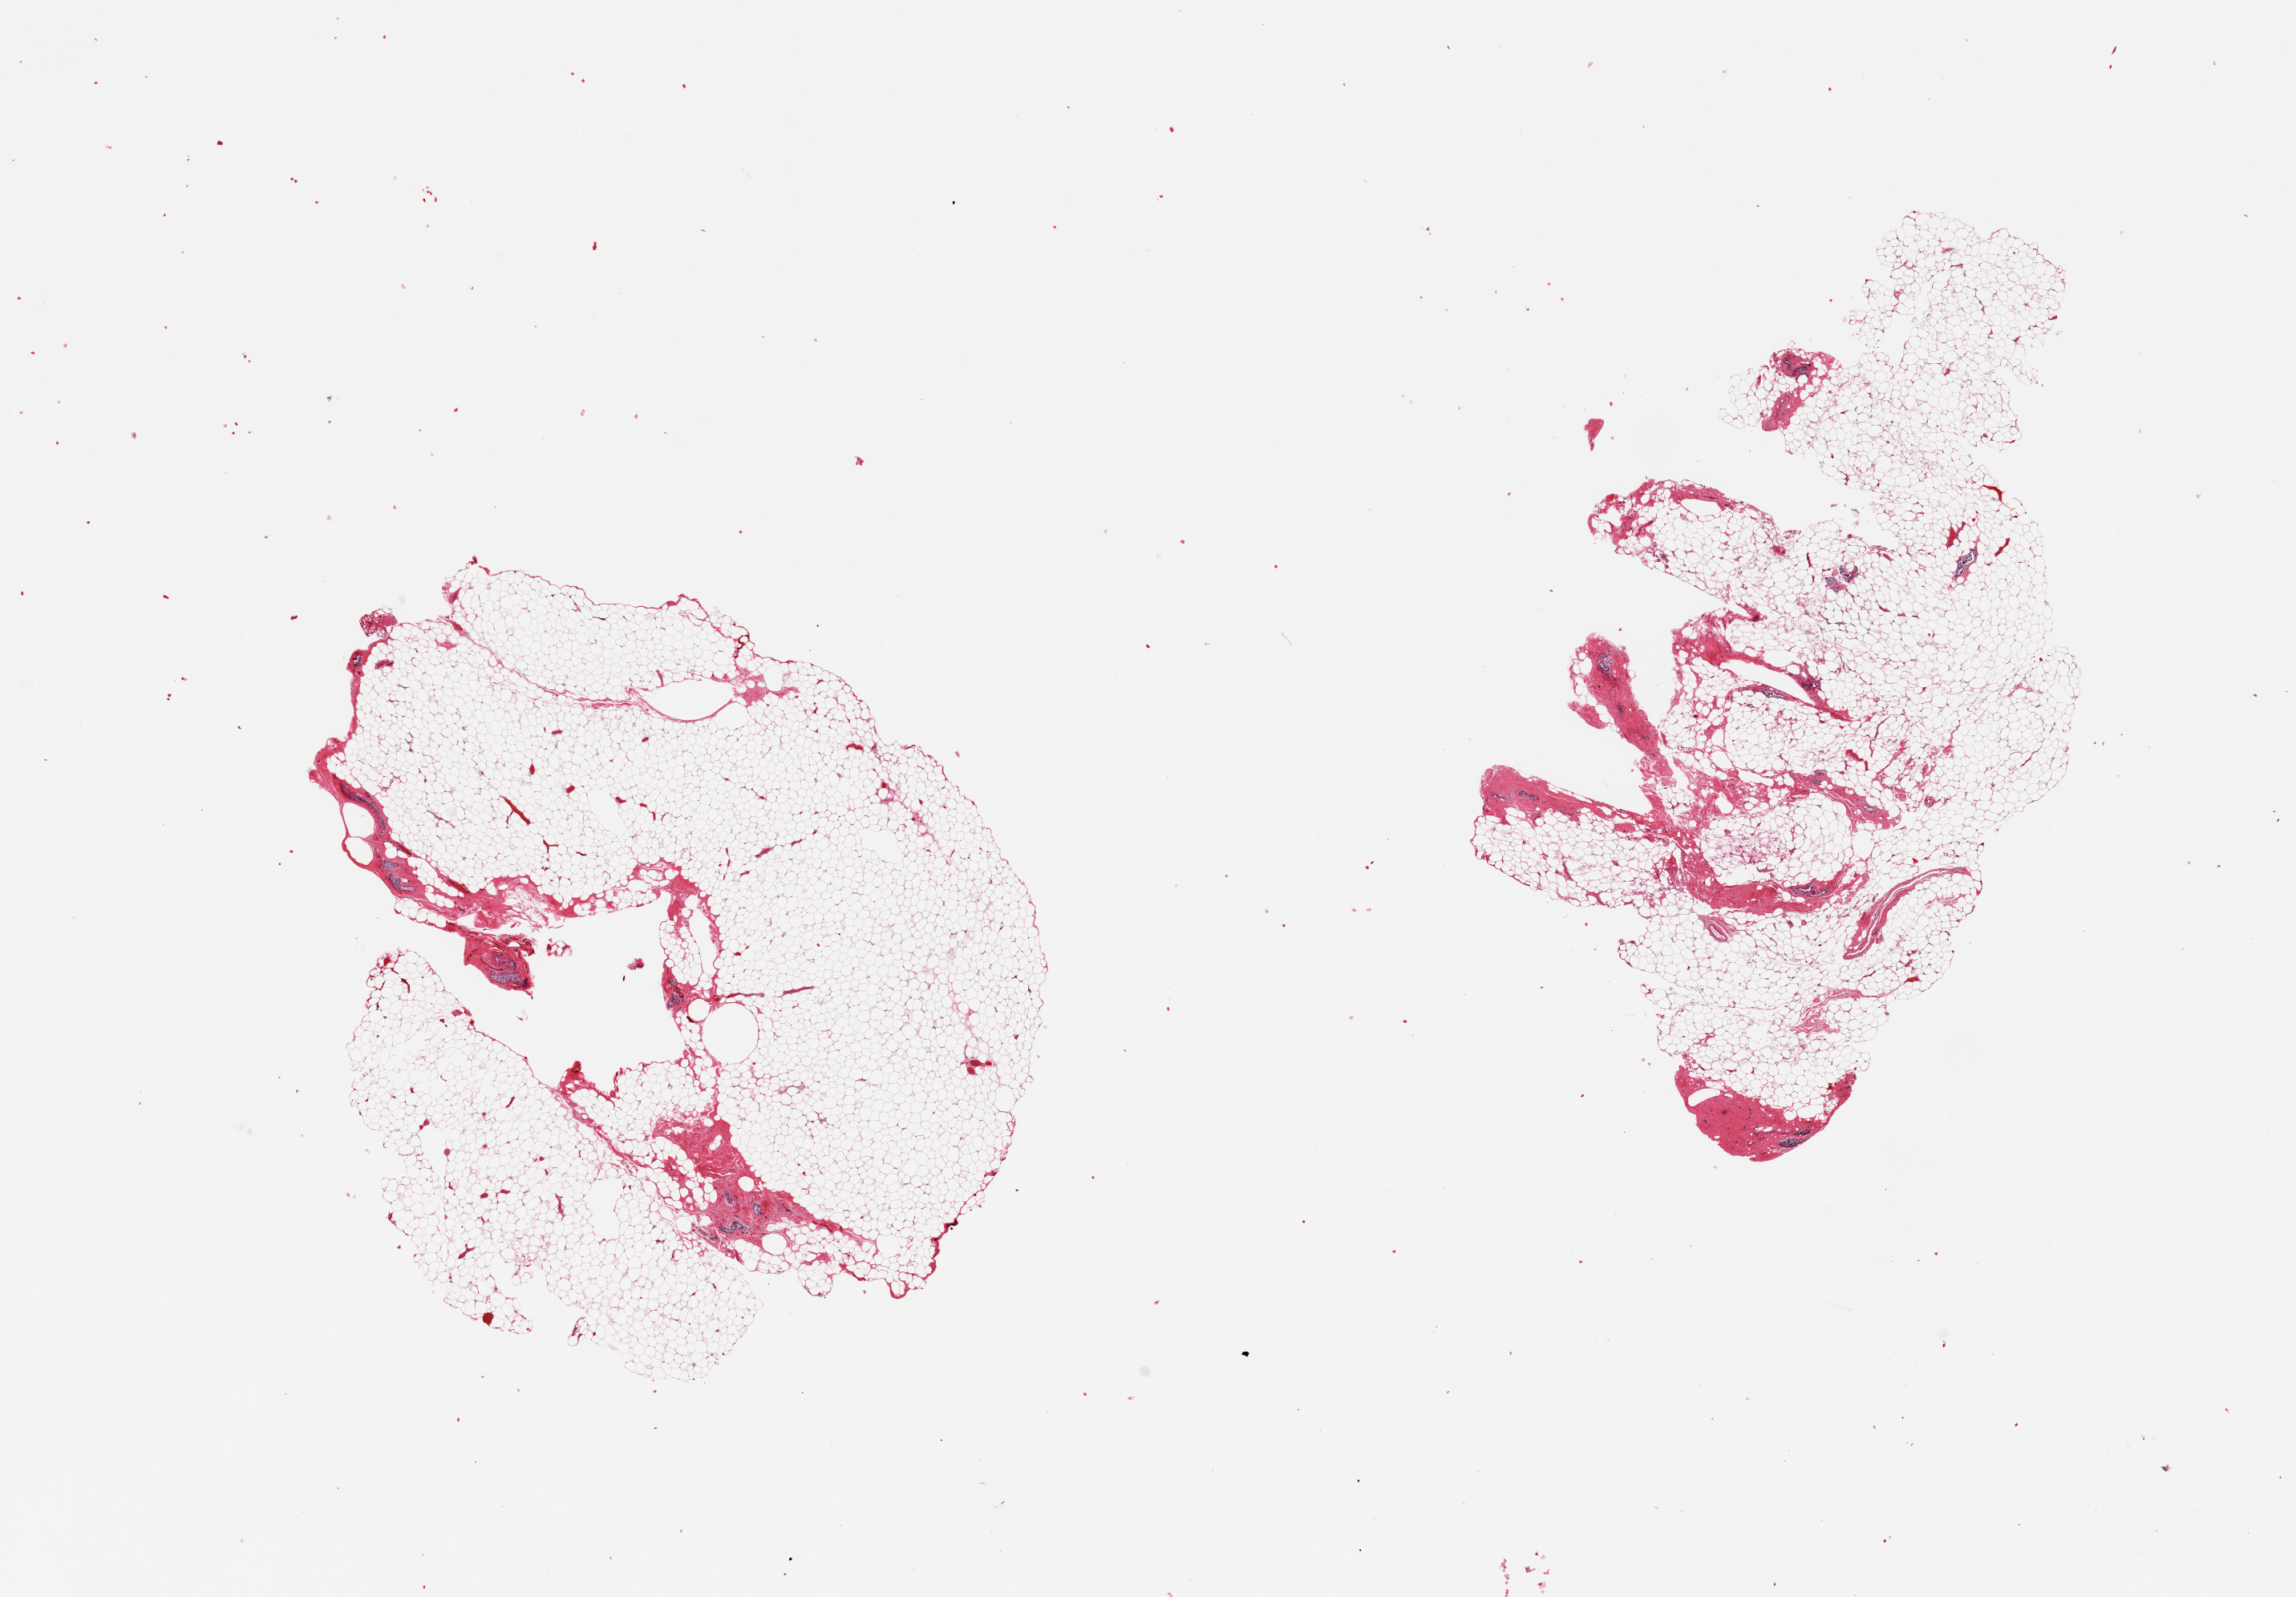
Digitized haematoxylin and eosin-stained section — shown as a low-resolution overview of the whole scanned area (about 22.6 x 15.8 mm, acquisition: 20x scan). PAXgene-fixed paraffin-embedded (PFPE) section. Section of breast (target tissue). Tissue donor sample. Donor sex: female.
- review note (as recorded): 2 pieces; atrophic ducts; most adipose